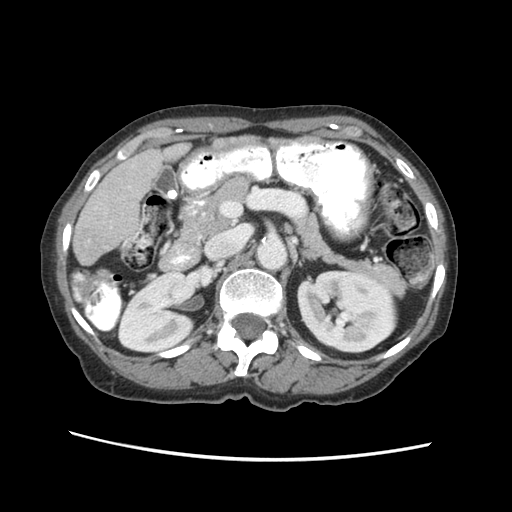
Contrast-enhanced abdominal CT (liver protocol), one axial slice. Slice 19 of 63 in the series (ordered by position). Reconstruction kernel STANDARD. 120 kVp. Soft-tissue window (W 400 / L 40 HU). 2.5 mm slice thickness. 512 × 512 image matrix. From the clinical record (not read from this slice): diagnosis: hepatocellular carcinoma (patient treated with transarterial chemoembolisation; whether this scan precedes or follows treatment is not stated here); TNM stage (as recorded): Stage-I; Child-Pugh class: B; tumour nodularity: uninodular.
Outlined on this slice (semi-automatic segmentation, software-assisted and operator-edited):
- liver parenchyma outside the tumour (the mass and vessels are separate outlines, so this box may not span the whole liver): box from (x=72, y=140) to (x=188, y=264) px